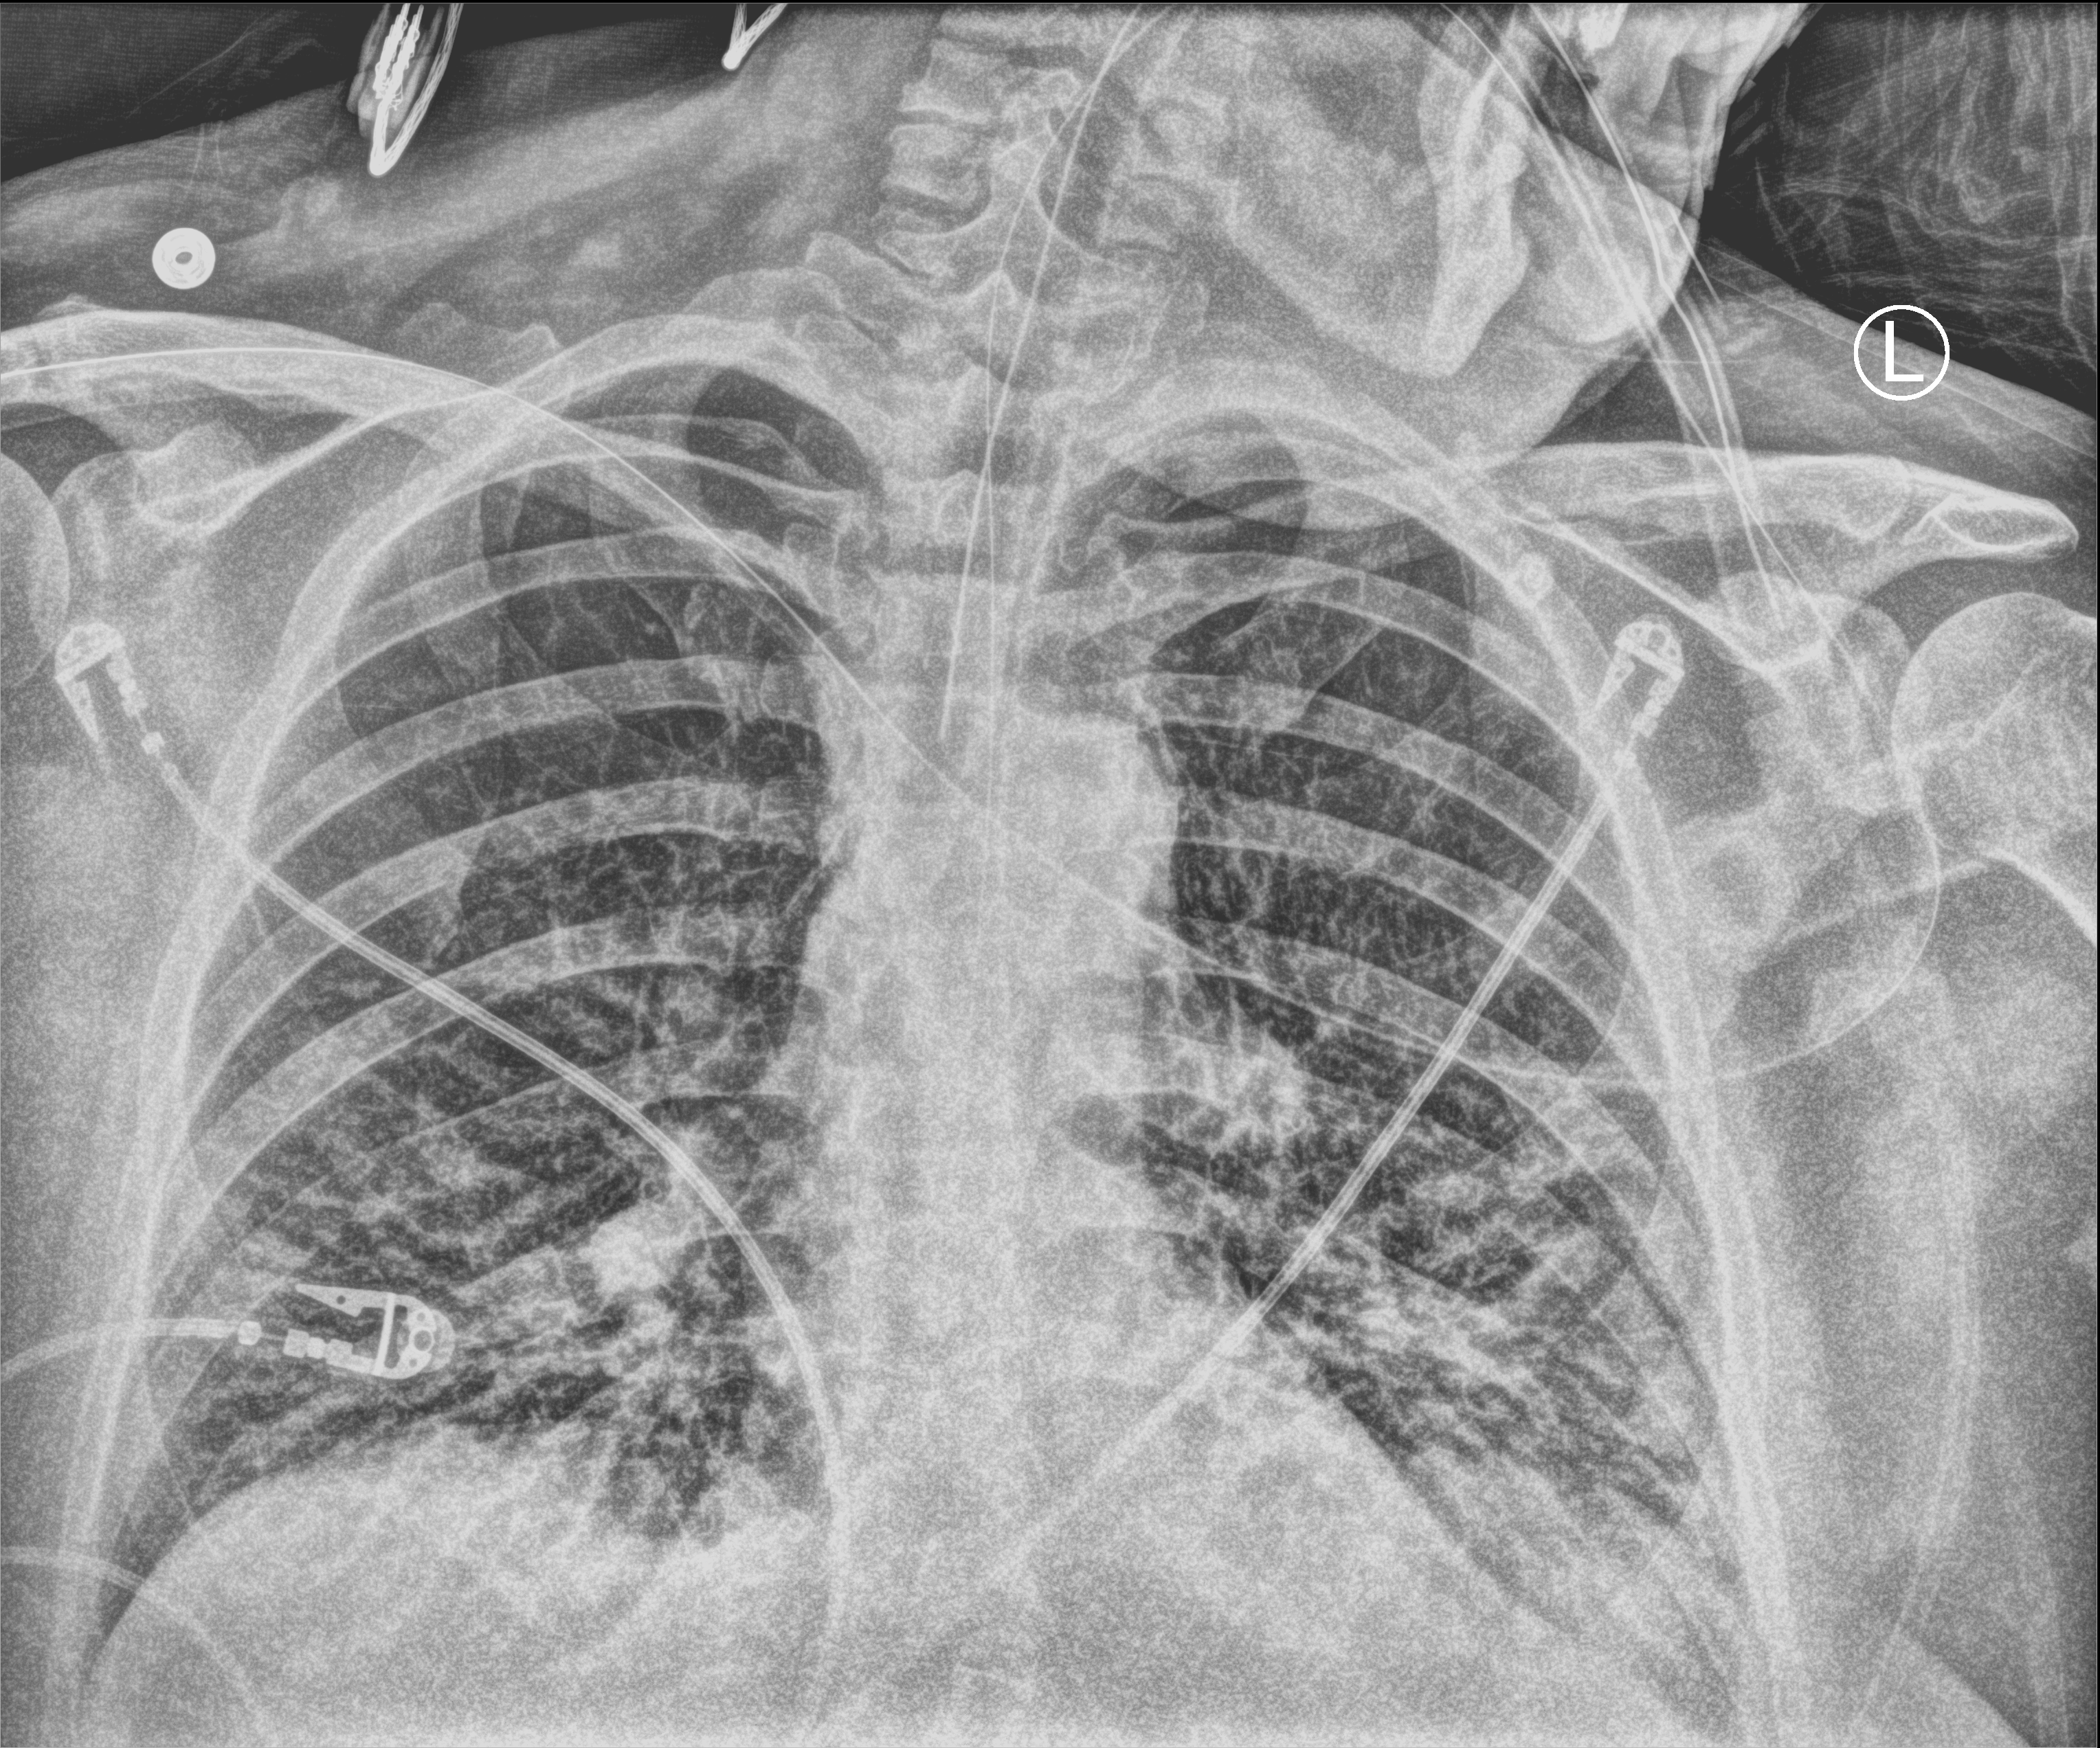
Portable chest radiograph; anteroposterior (AP) projection. Patient hospitalised with COVID-19, aged 18–59 years.
Admission-level facts for this patient (not findings on this image; timing relative to this image not recorded):
- admitted to intensive care during this hospital stay: yes
- length of hospital stay: 9 days